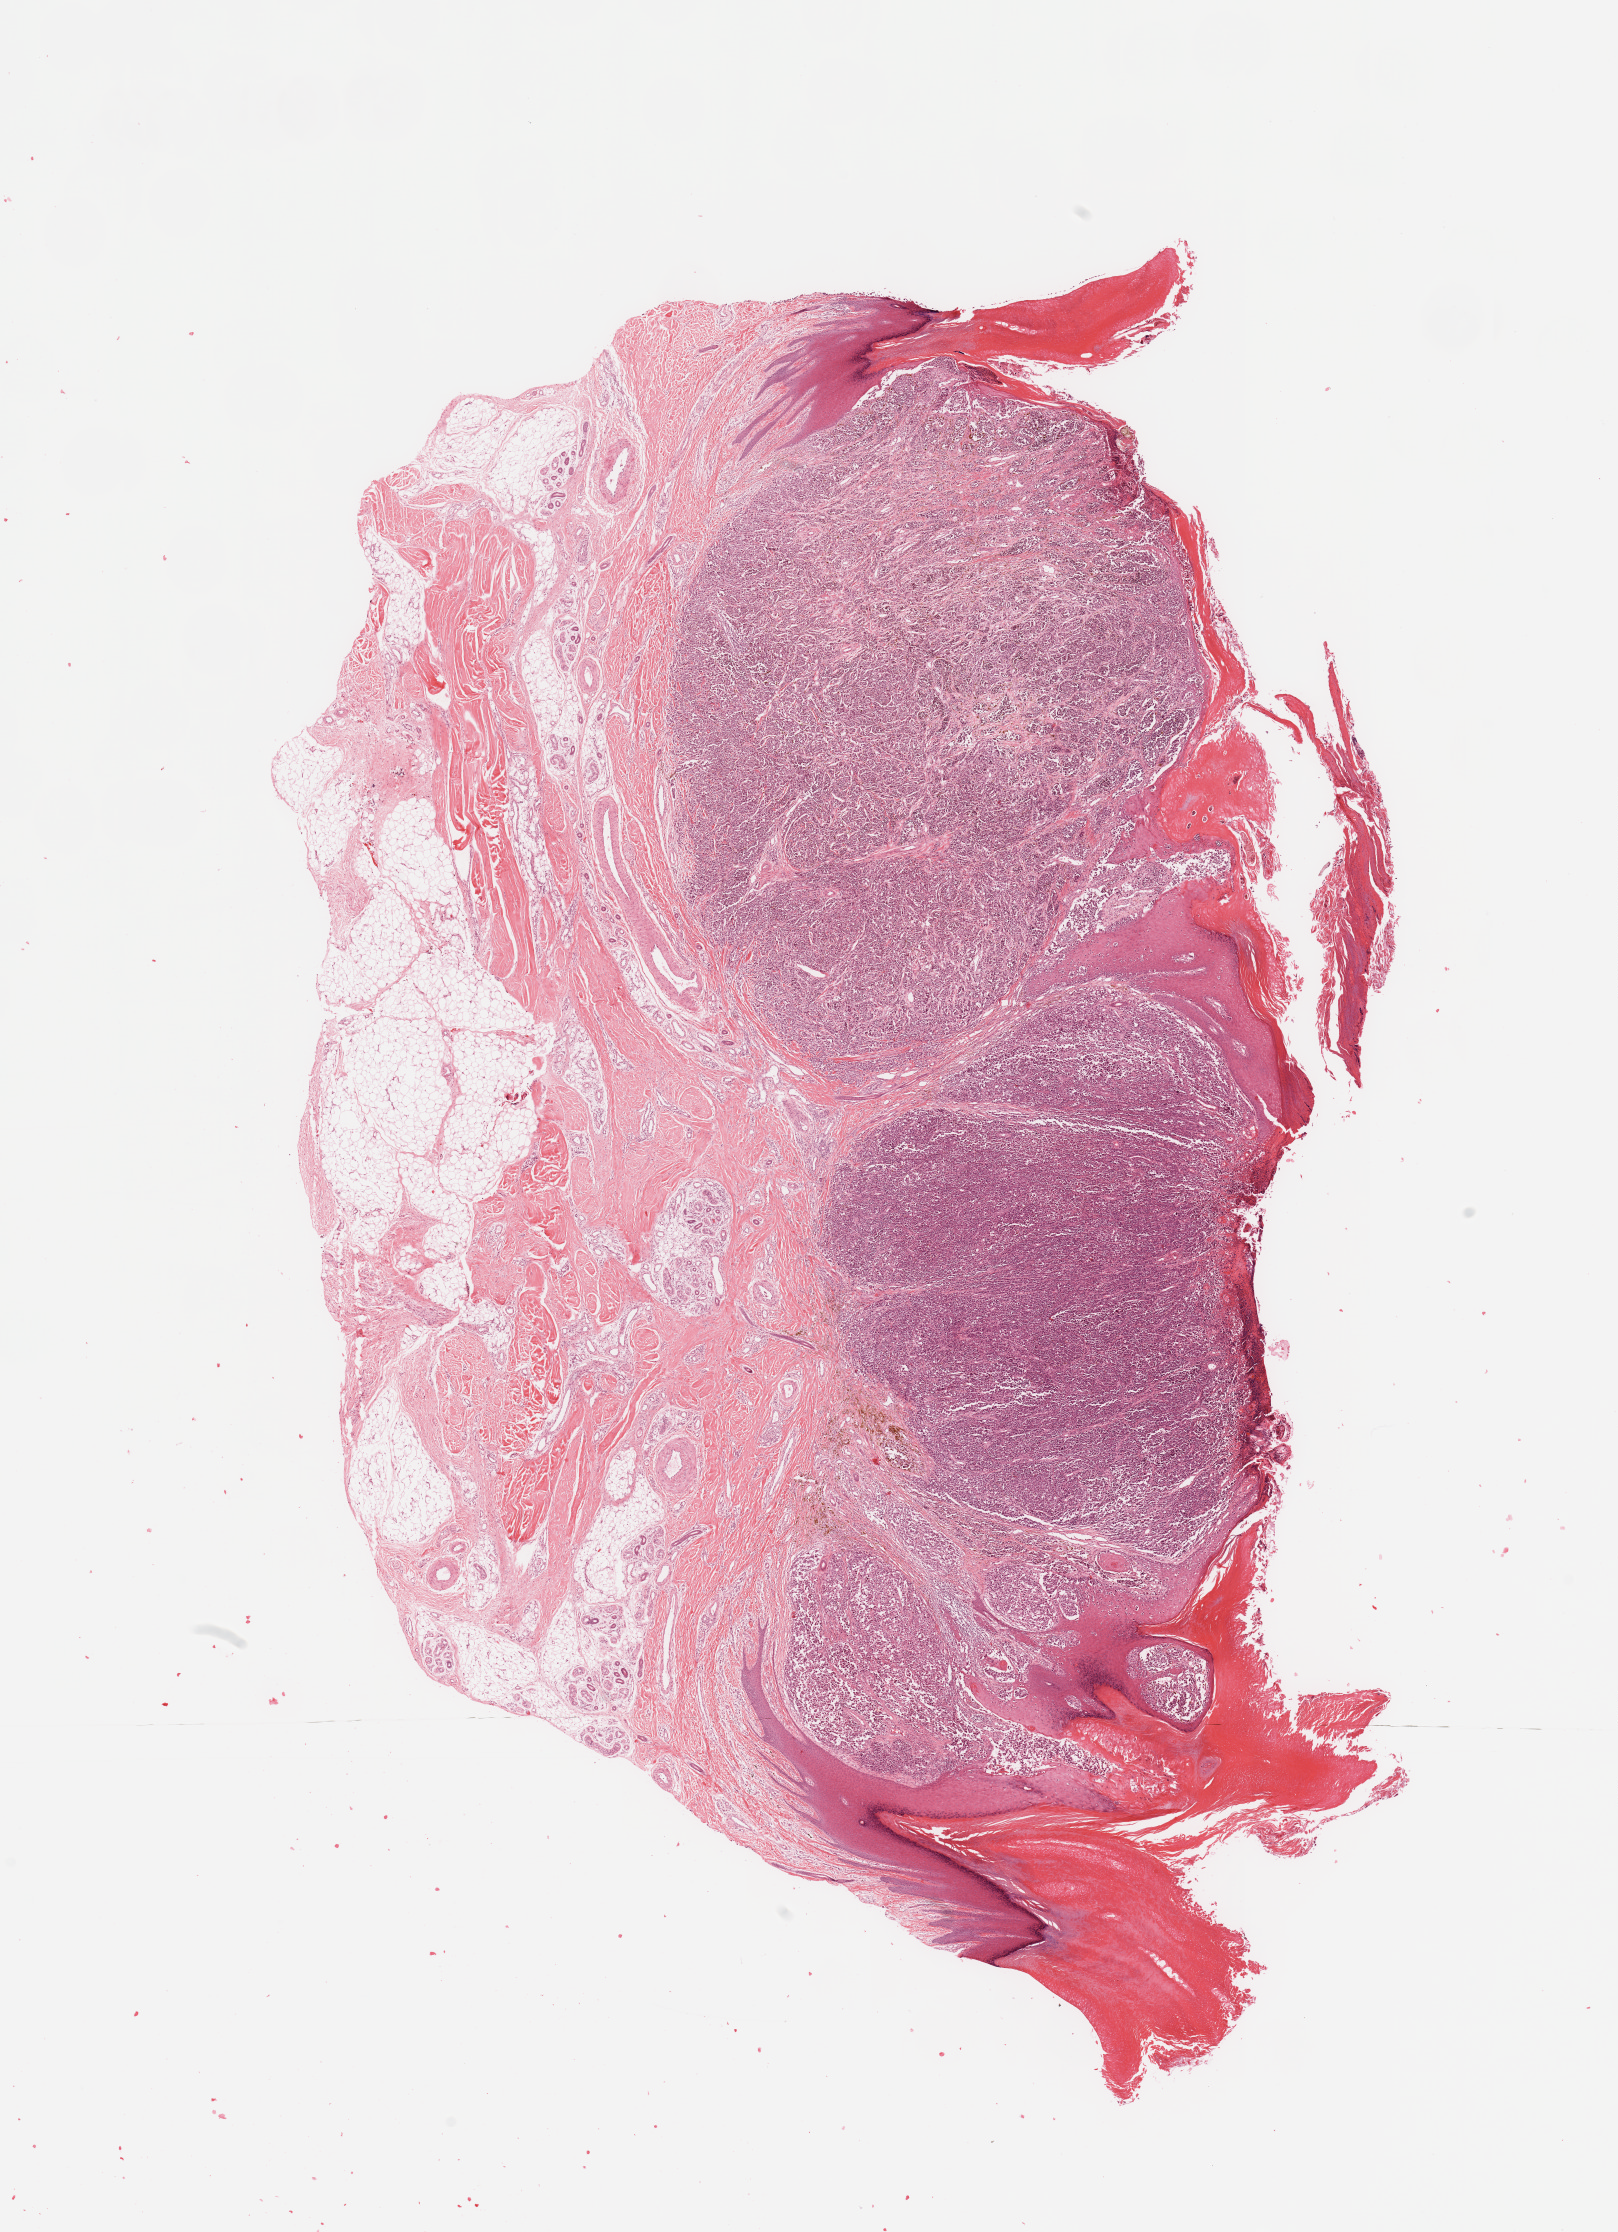
H&E-stained whole-slide image, whole scanned area (about 12.8 x 17.7 mm) shown as a low-resolution overview. Melanoma tumour tissue; sampled site not recorded. 69-year-old male patient.
• histologic diagnosis: Malignant melanoma, NOS
• AJCC pathologic stage: IIIC